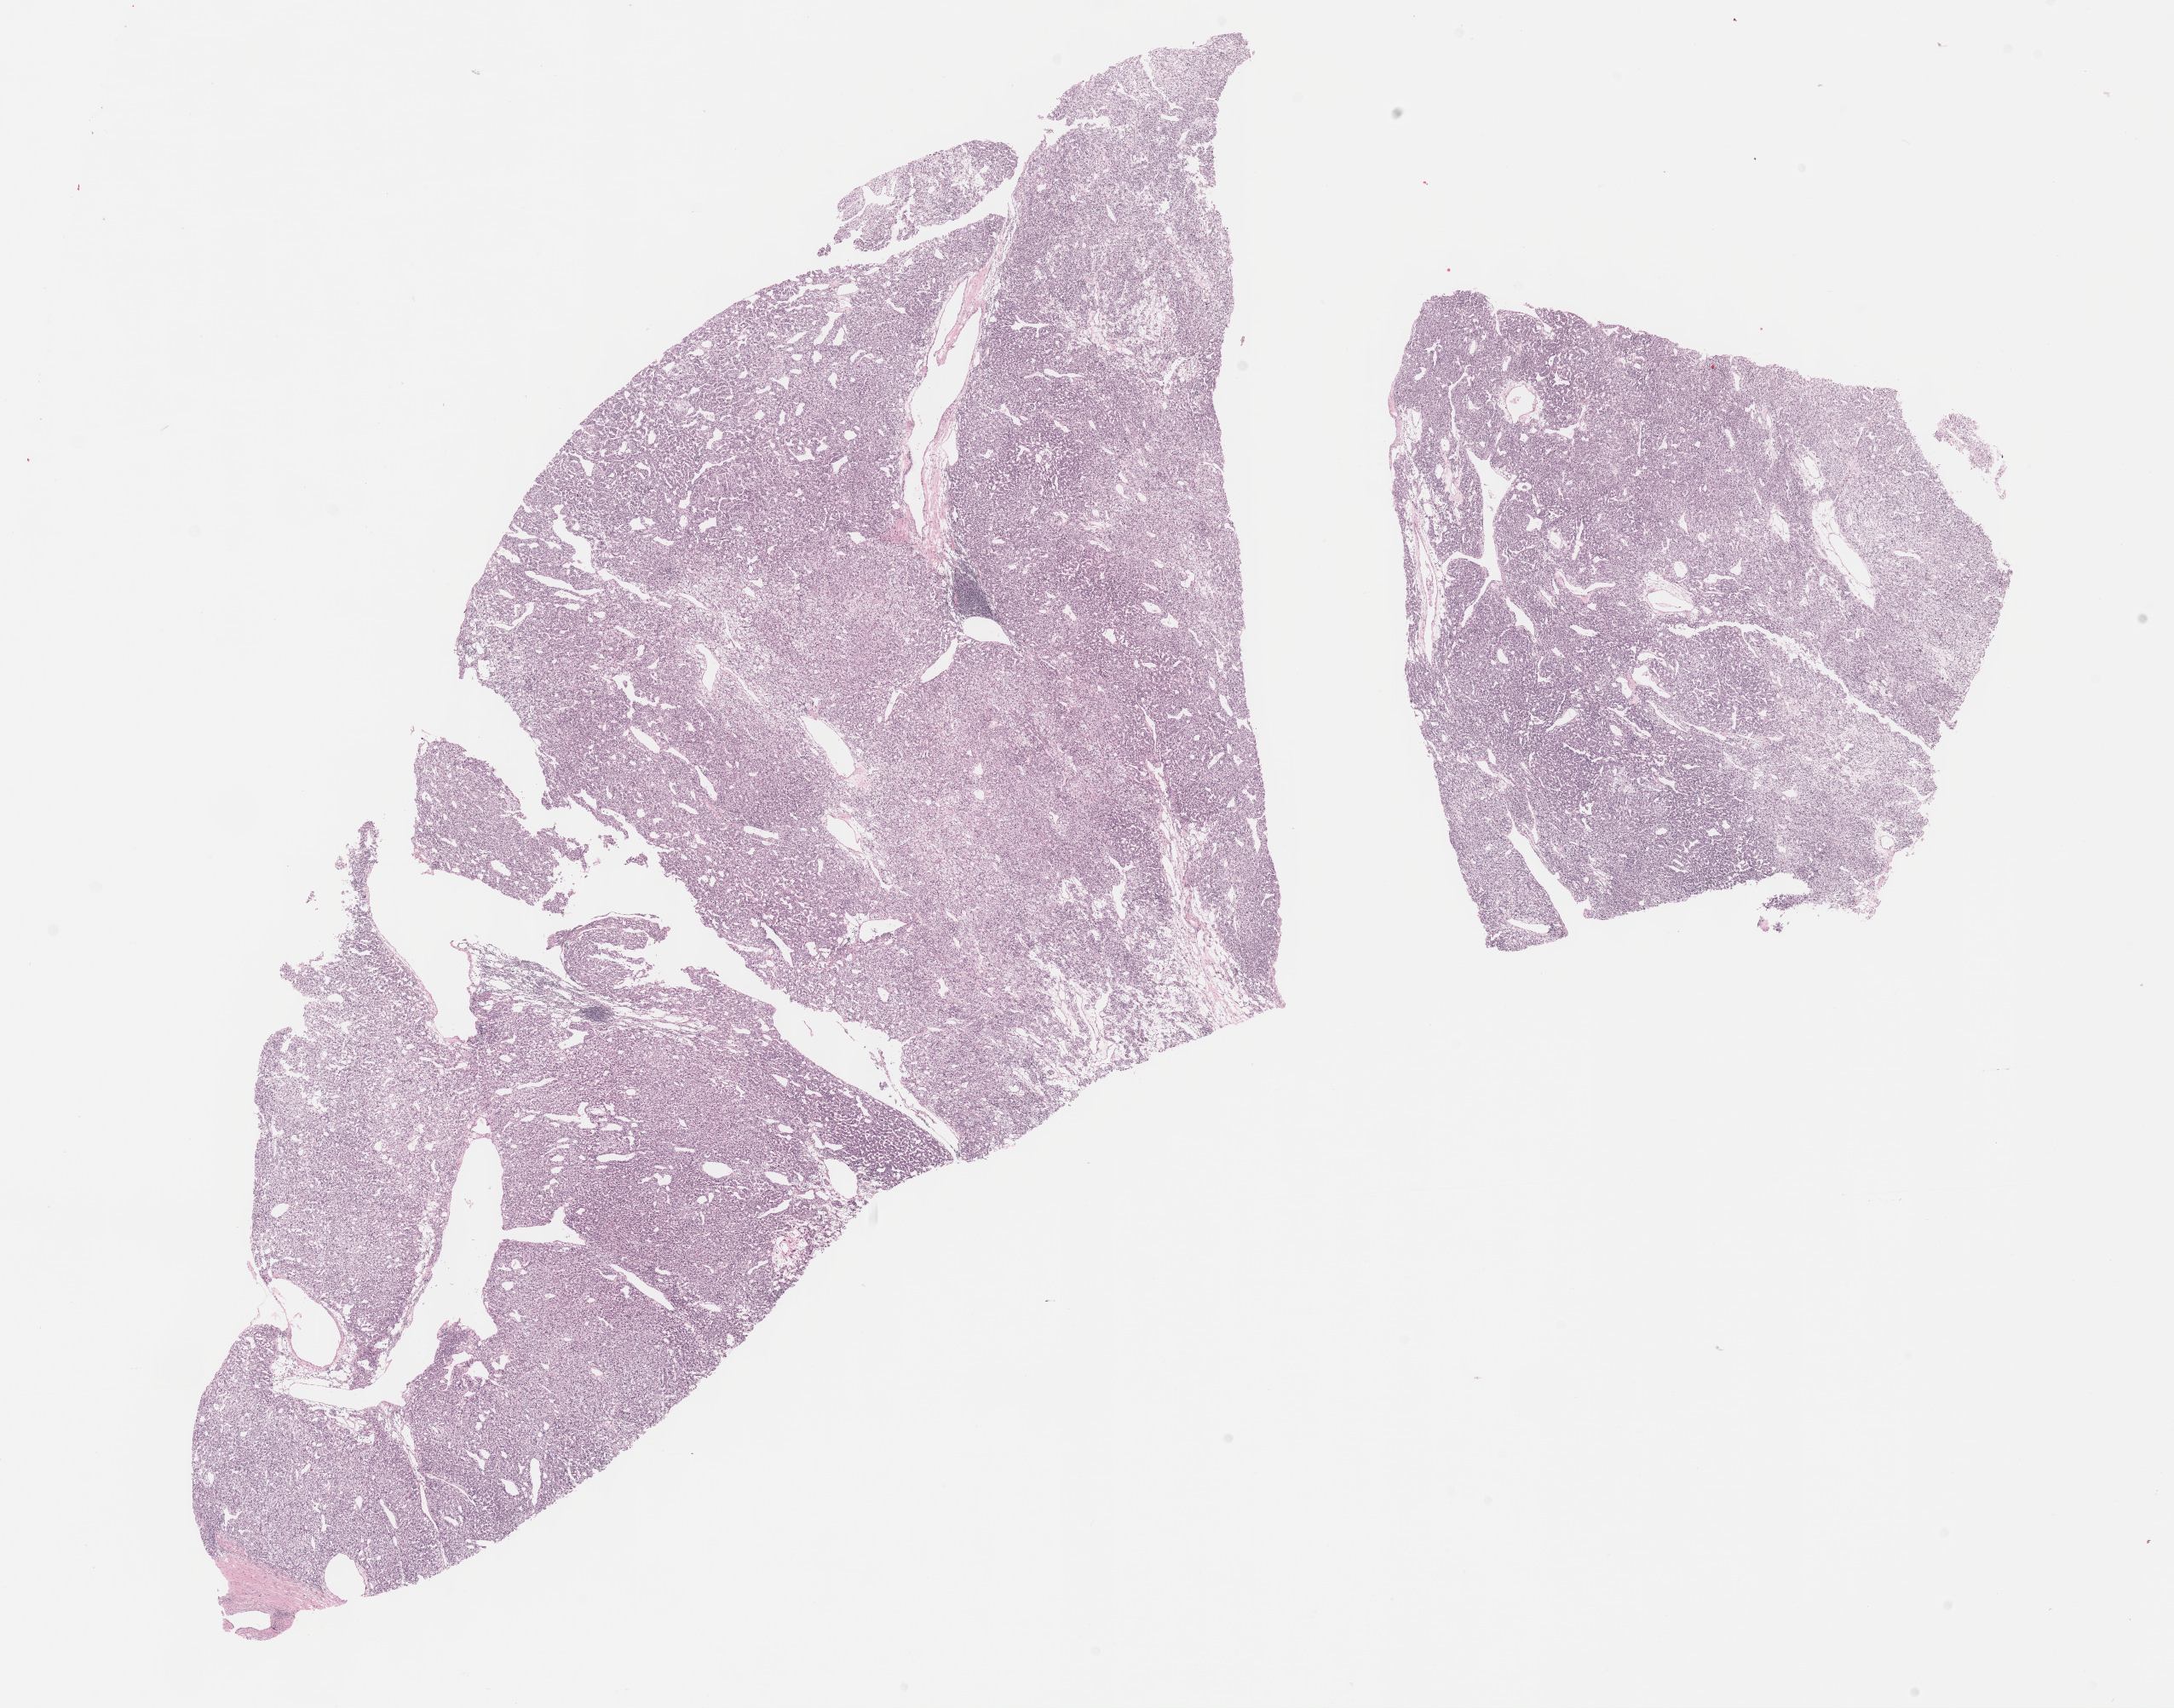
H&E whole-slide image — a low-resolution overview of the entire scanned area, about 20.6 x 16.2 mm; FFPE section; primary tumour sample from the kidney. Female, age 54 years at initial diagnosis. Histologic grade: G2 (moderately differentiated).
• TNM: T2 N0 M0
• AJCC pathologic stage: II (7th edition)
• lymph nodes positive (case pathology): 0 of 5 examined
• laterality: right
• diagnosis: Clear cell adenocarcinoma, NOS